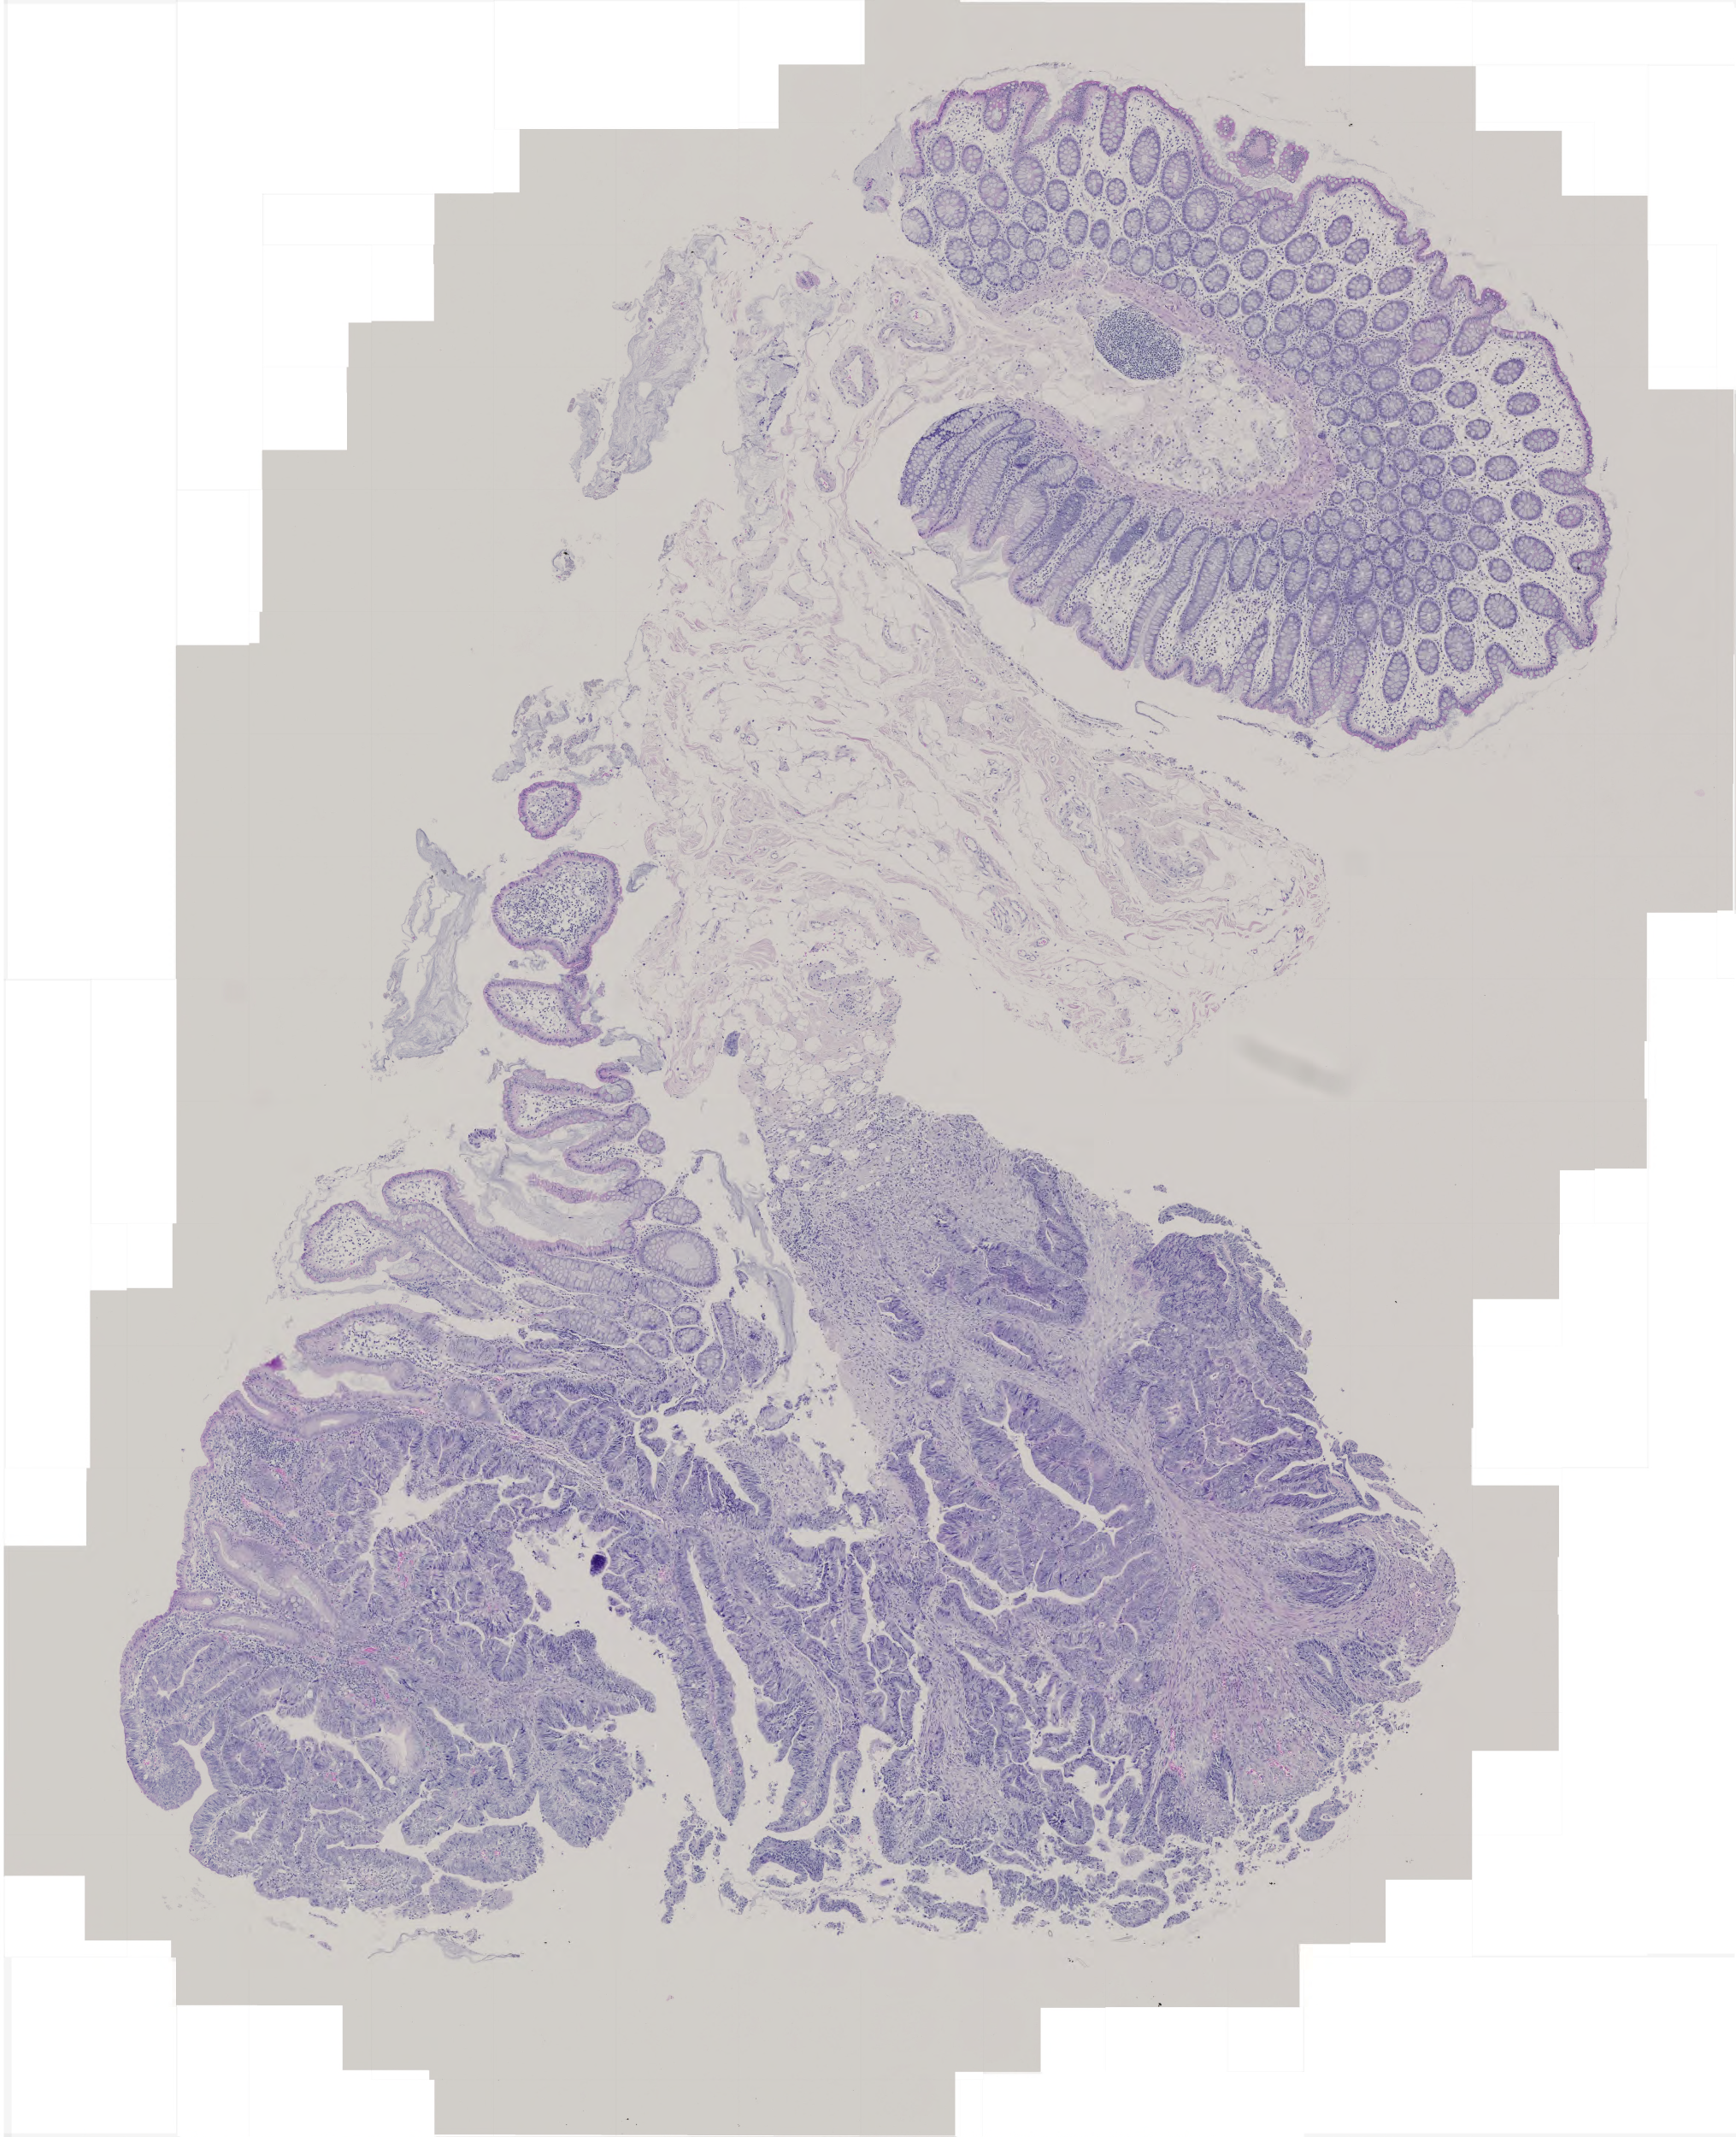
Whole-slide histology image, H&E — whole scanned area (about 4.1 x 5.0 mm) shown as a low-resolution overview. Formalin-fixed paraffin-embedded (FFPE) diagnostic section. Sample: primary tumour, colon. Male patient; age at initial diagnosis 79 years.
Pathologic diagnosis: Adenocarcinoma, NOS (ascending colon).